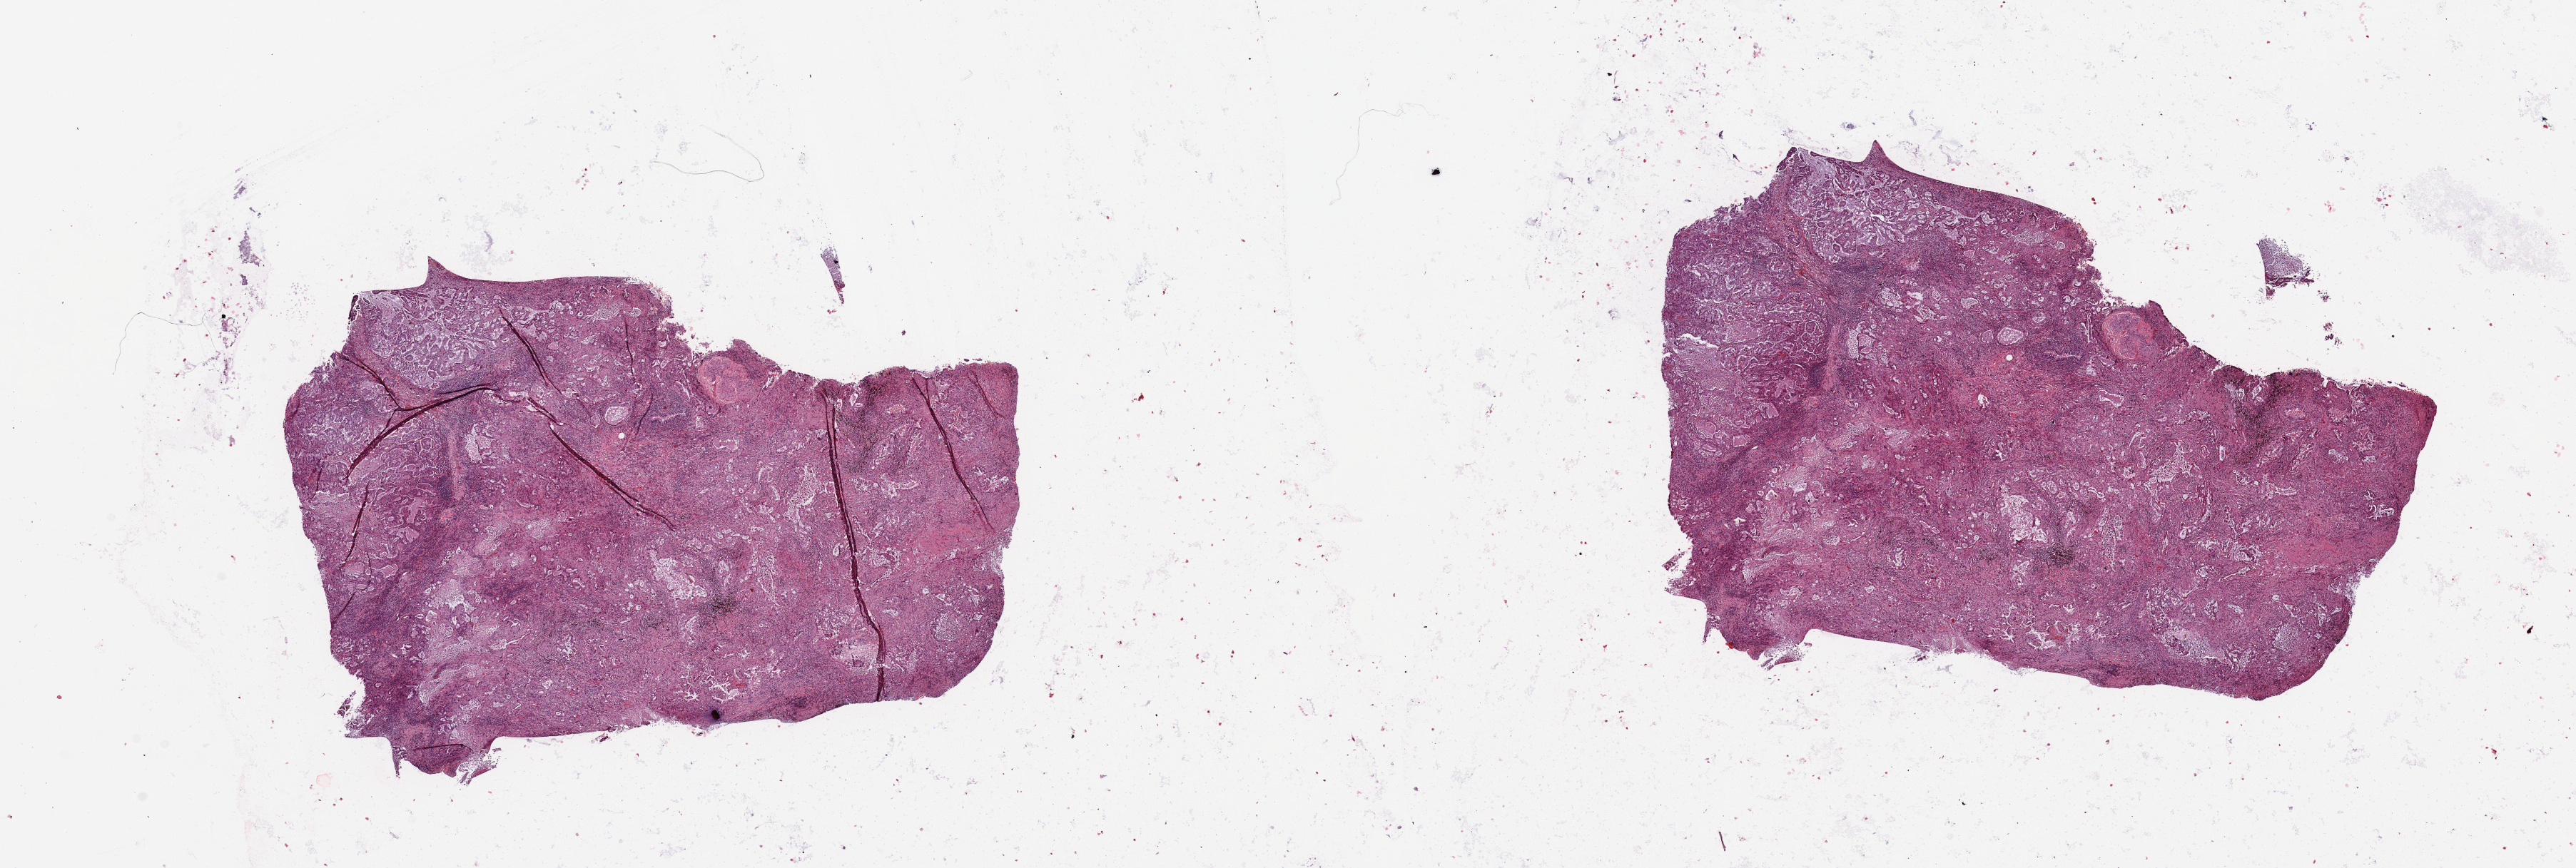
H&E-stained whole-slide image — a low-resolution overview of the entire scanned area, about 28.5 x 9.6 mm (from a 20x scan). Lung, tumour tissue. 70-year-old female patient. Histologic grade: G1 (well differentiated).
Histologic diagnosis: Adenocarcinoma, NOS. AJCC pathologic stage: IIIA.